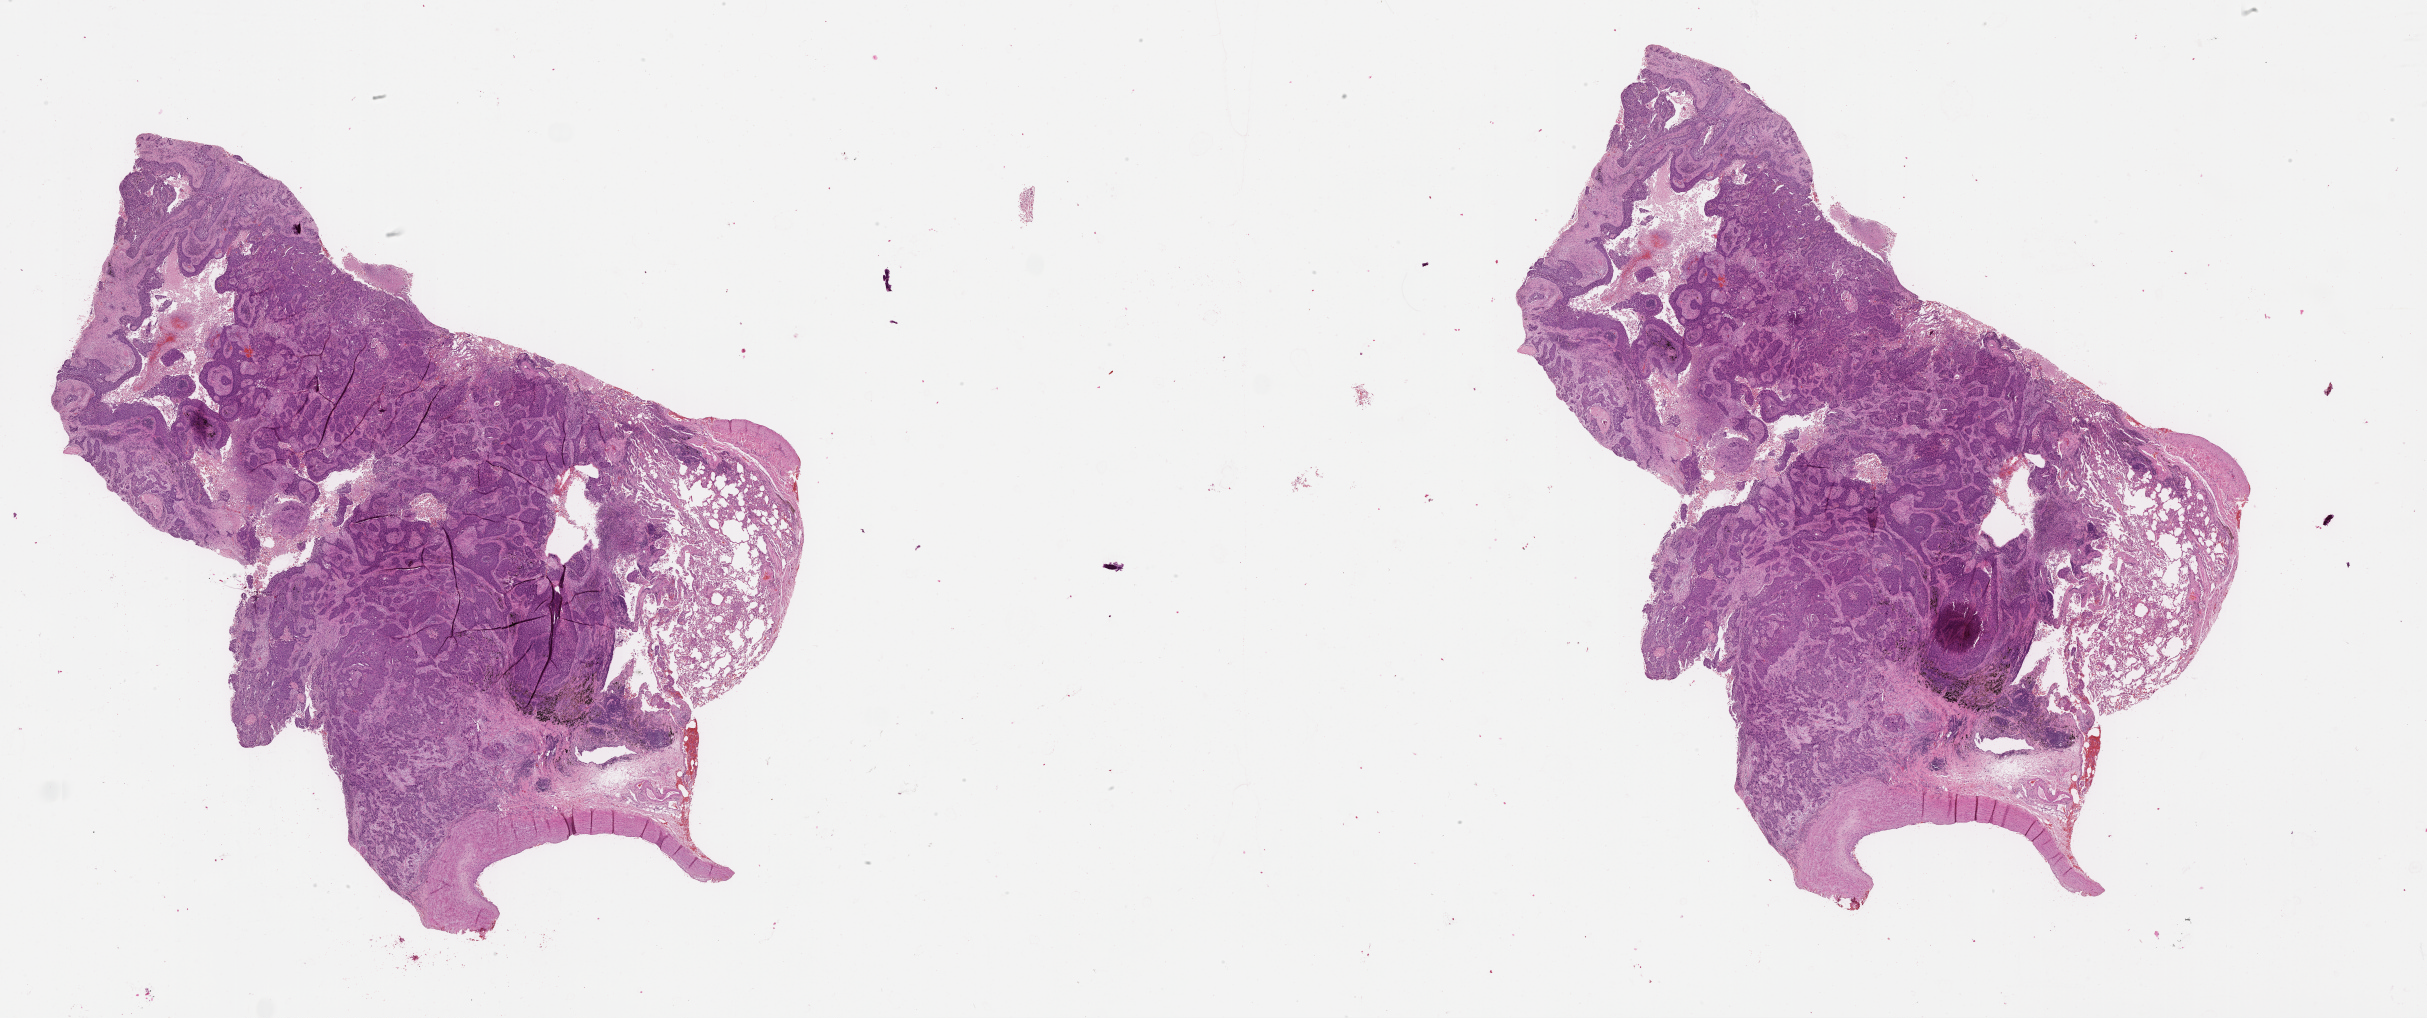
H&E whole-slide image — low-resolution overview of the scanned area, about 39.1 x 16.4 mm (from a 20x scan), tumour tissue sample, lung. Male, 59 y/o.
Patient diagnosis (cohort enrolment): squamous cell carcinoma (lung).